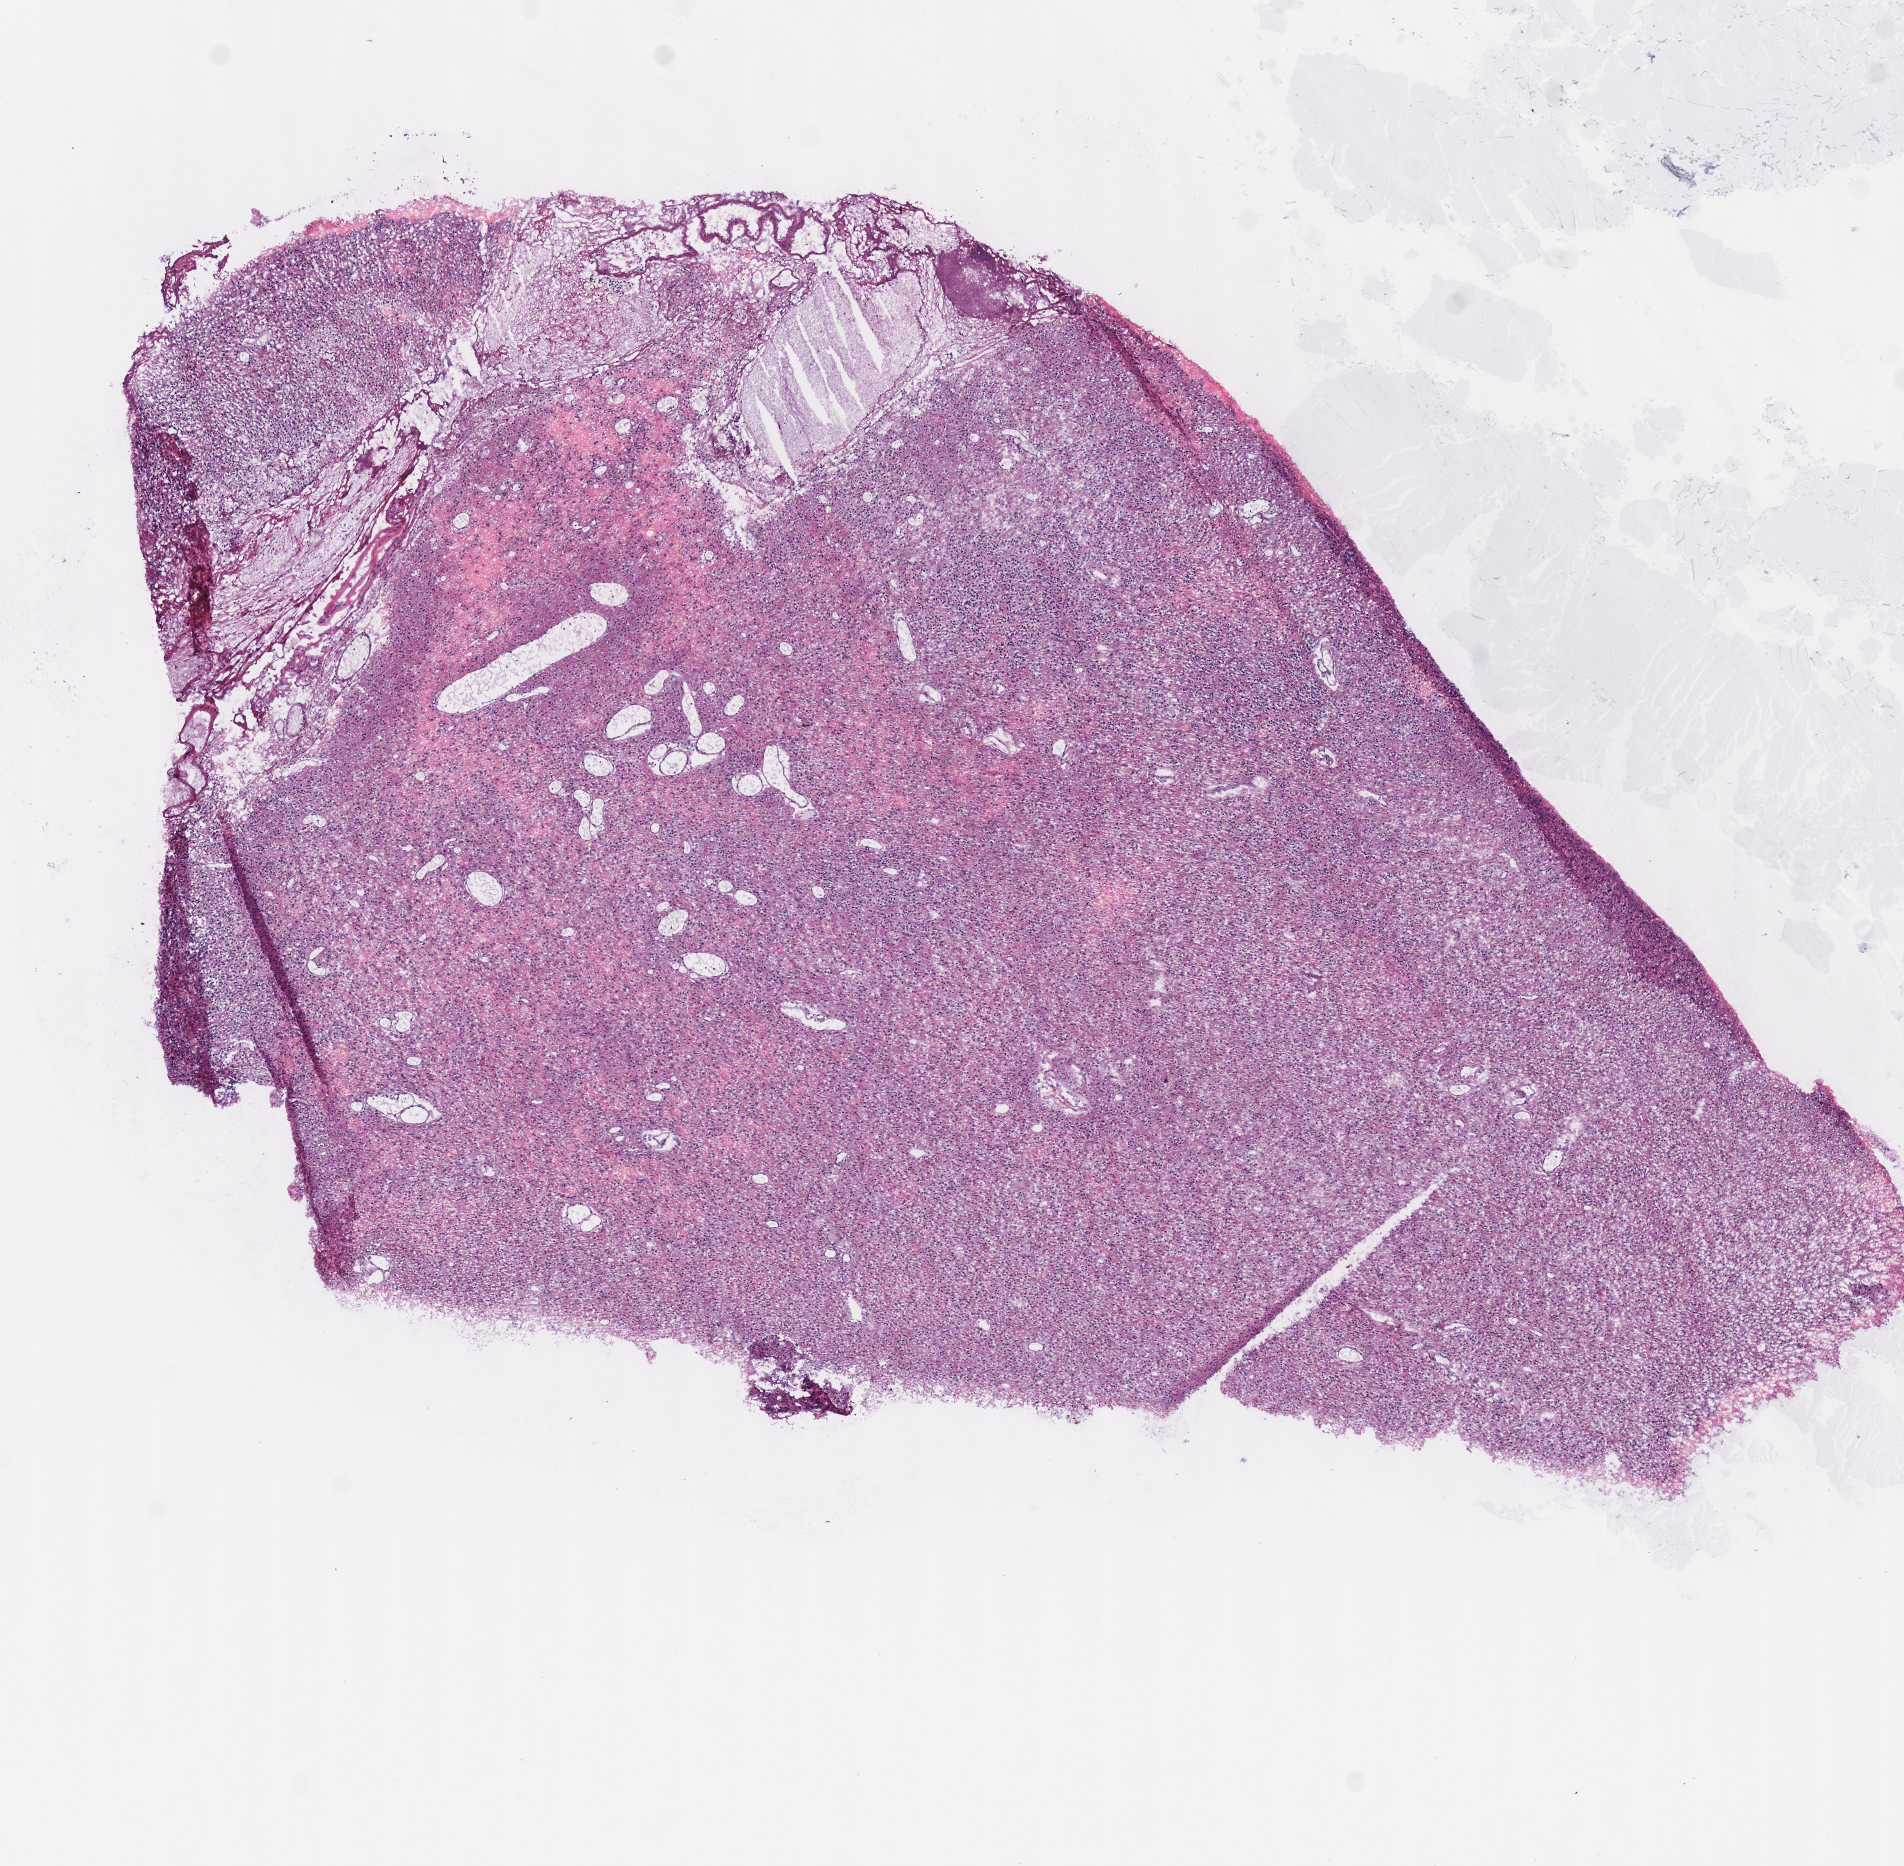
Digitized Hematoxylin and eosin (H&E) stained tissue section (whole slide), shown as a low-resolution overview of the whole scanned area (about 7.5 x 7.4 mm, acquisition: 40x scan), frozen section from the top of the tissue portion, brain, primary tumour sample. Patient: male, age at initial diagnosis 53 years. Histologic grade: G3 (poorly differentiated). Composition of this section per pathologist review: tumour cells 95%, tumour nuclei 80%, normal cells 0%, stromal cells 5%, necrosis 0%.
- histologic diagnosis: Oligodendroglioma, anaplastic (cerebrum)